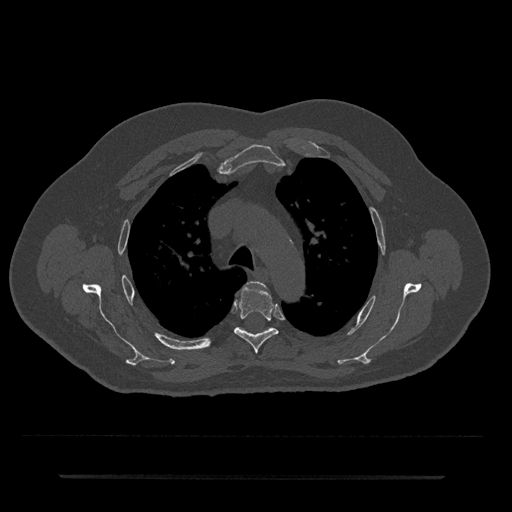
CT including the spine, one axial slice; position 525 of 797 along the scan axis; reconstruction kernel Br40s/3; 120 kVp; bone window (W 1800 / L 400 HU); 0.5 mm slice thickness; 512 × 512 image matrix, field of view 437 × 437 mm. Patient: male, 69 years. Case-level facts recorded for this patient, not image findings: primary cancer: prostate.
Outlined on this slice (semi-automatically segmented with operator editing):
- T4 vertebra: bounding box (x1, y1, x2, y2) in pixels: (234, 287, 278, 354)
- T5 vertebra: (238, 327, 271, 332)